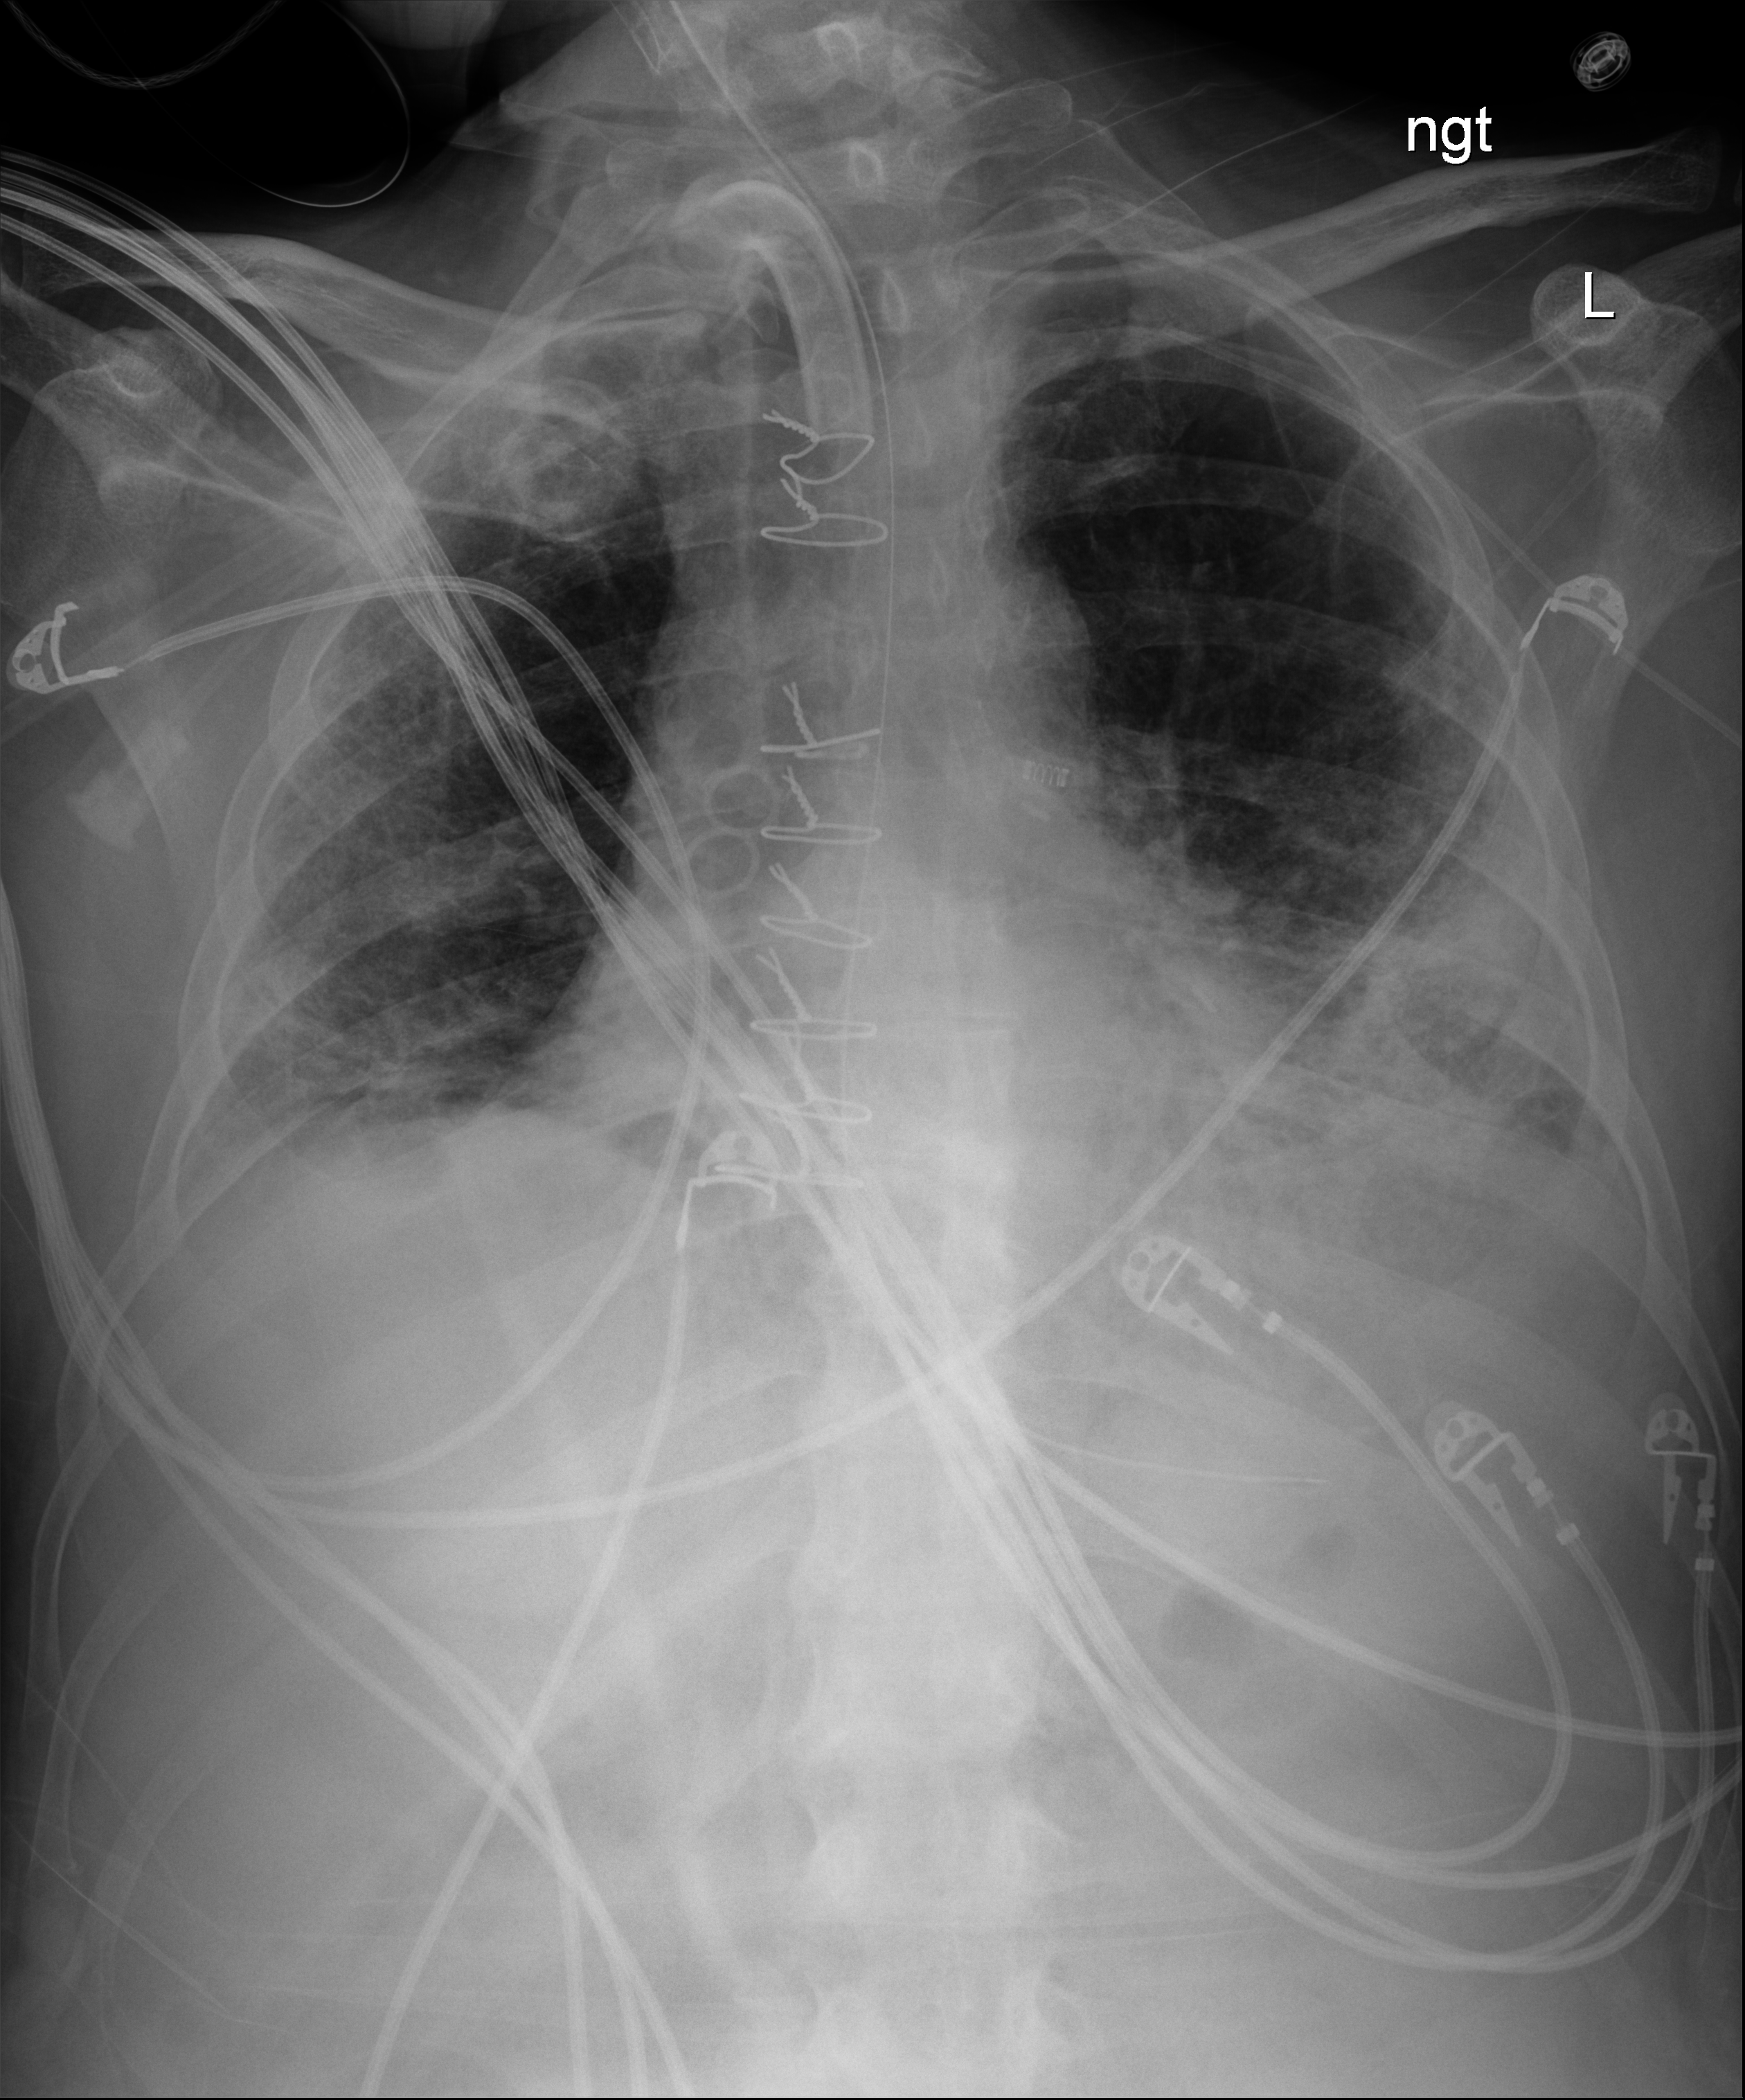
Chest radiograph (digital radiography), anteroposterior (AP) projection. Male patient hospitalised with COVID-19, age 18–59 years.
Hospital-stay facts (about this admission, not read from this image; timing relative to this image not recorded):
- hypertension (admission record): no